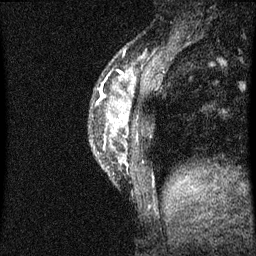
Breast MRI (dynamic contrast-enhanced), one sagittal slice; position 15 of 60 along the scan axis; dynamic contrast-enhanced series, image 2 of 3 at this slice position (ordered by acquisition); 1.5 T; TE 4.2 ms, TR 8 ms; 2 mm slice thickness; 256 × 256 image matrix, field of view 180 × 180 mm. Patient: female, 33 years.
Annotated regions visible in this slice (semi-automatically segmented with operator editing):
- analysis volume of interest (the breast-tissue region the enhancement analysis was run in; not a lesion): bounding box (x1, y1, x2, y2) in pixels: (90, 72, 151, 187)
- tumour enhancement mask (voxels above the 70 % enhancement threshold inside the analysis volume of interest): (120, 116, 125, 119)